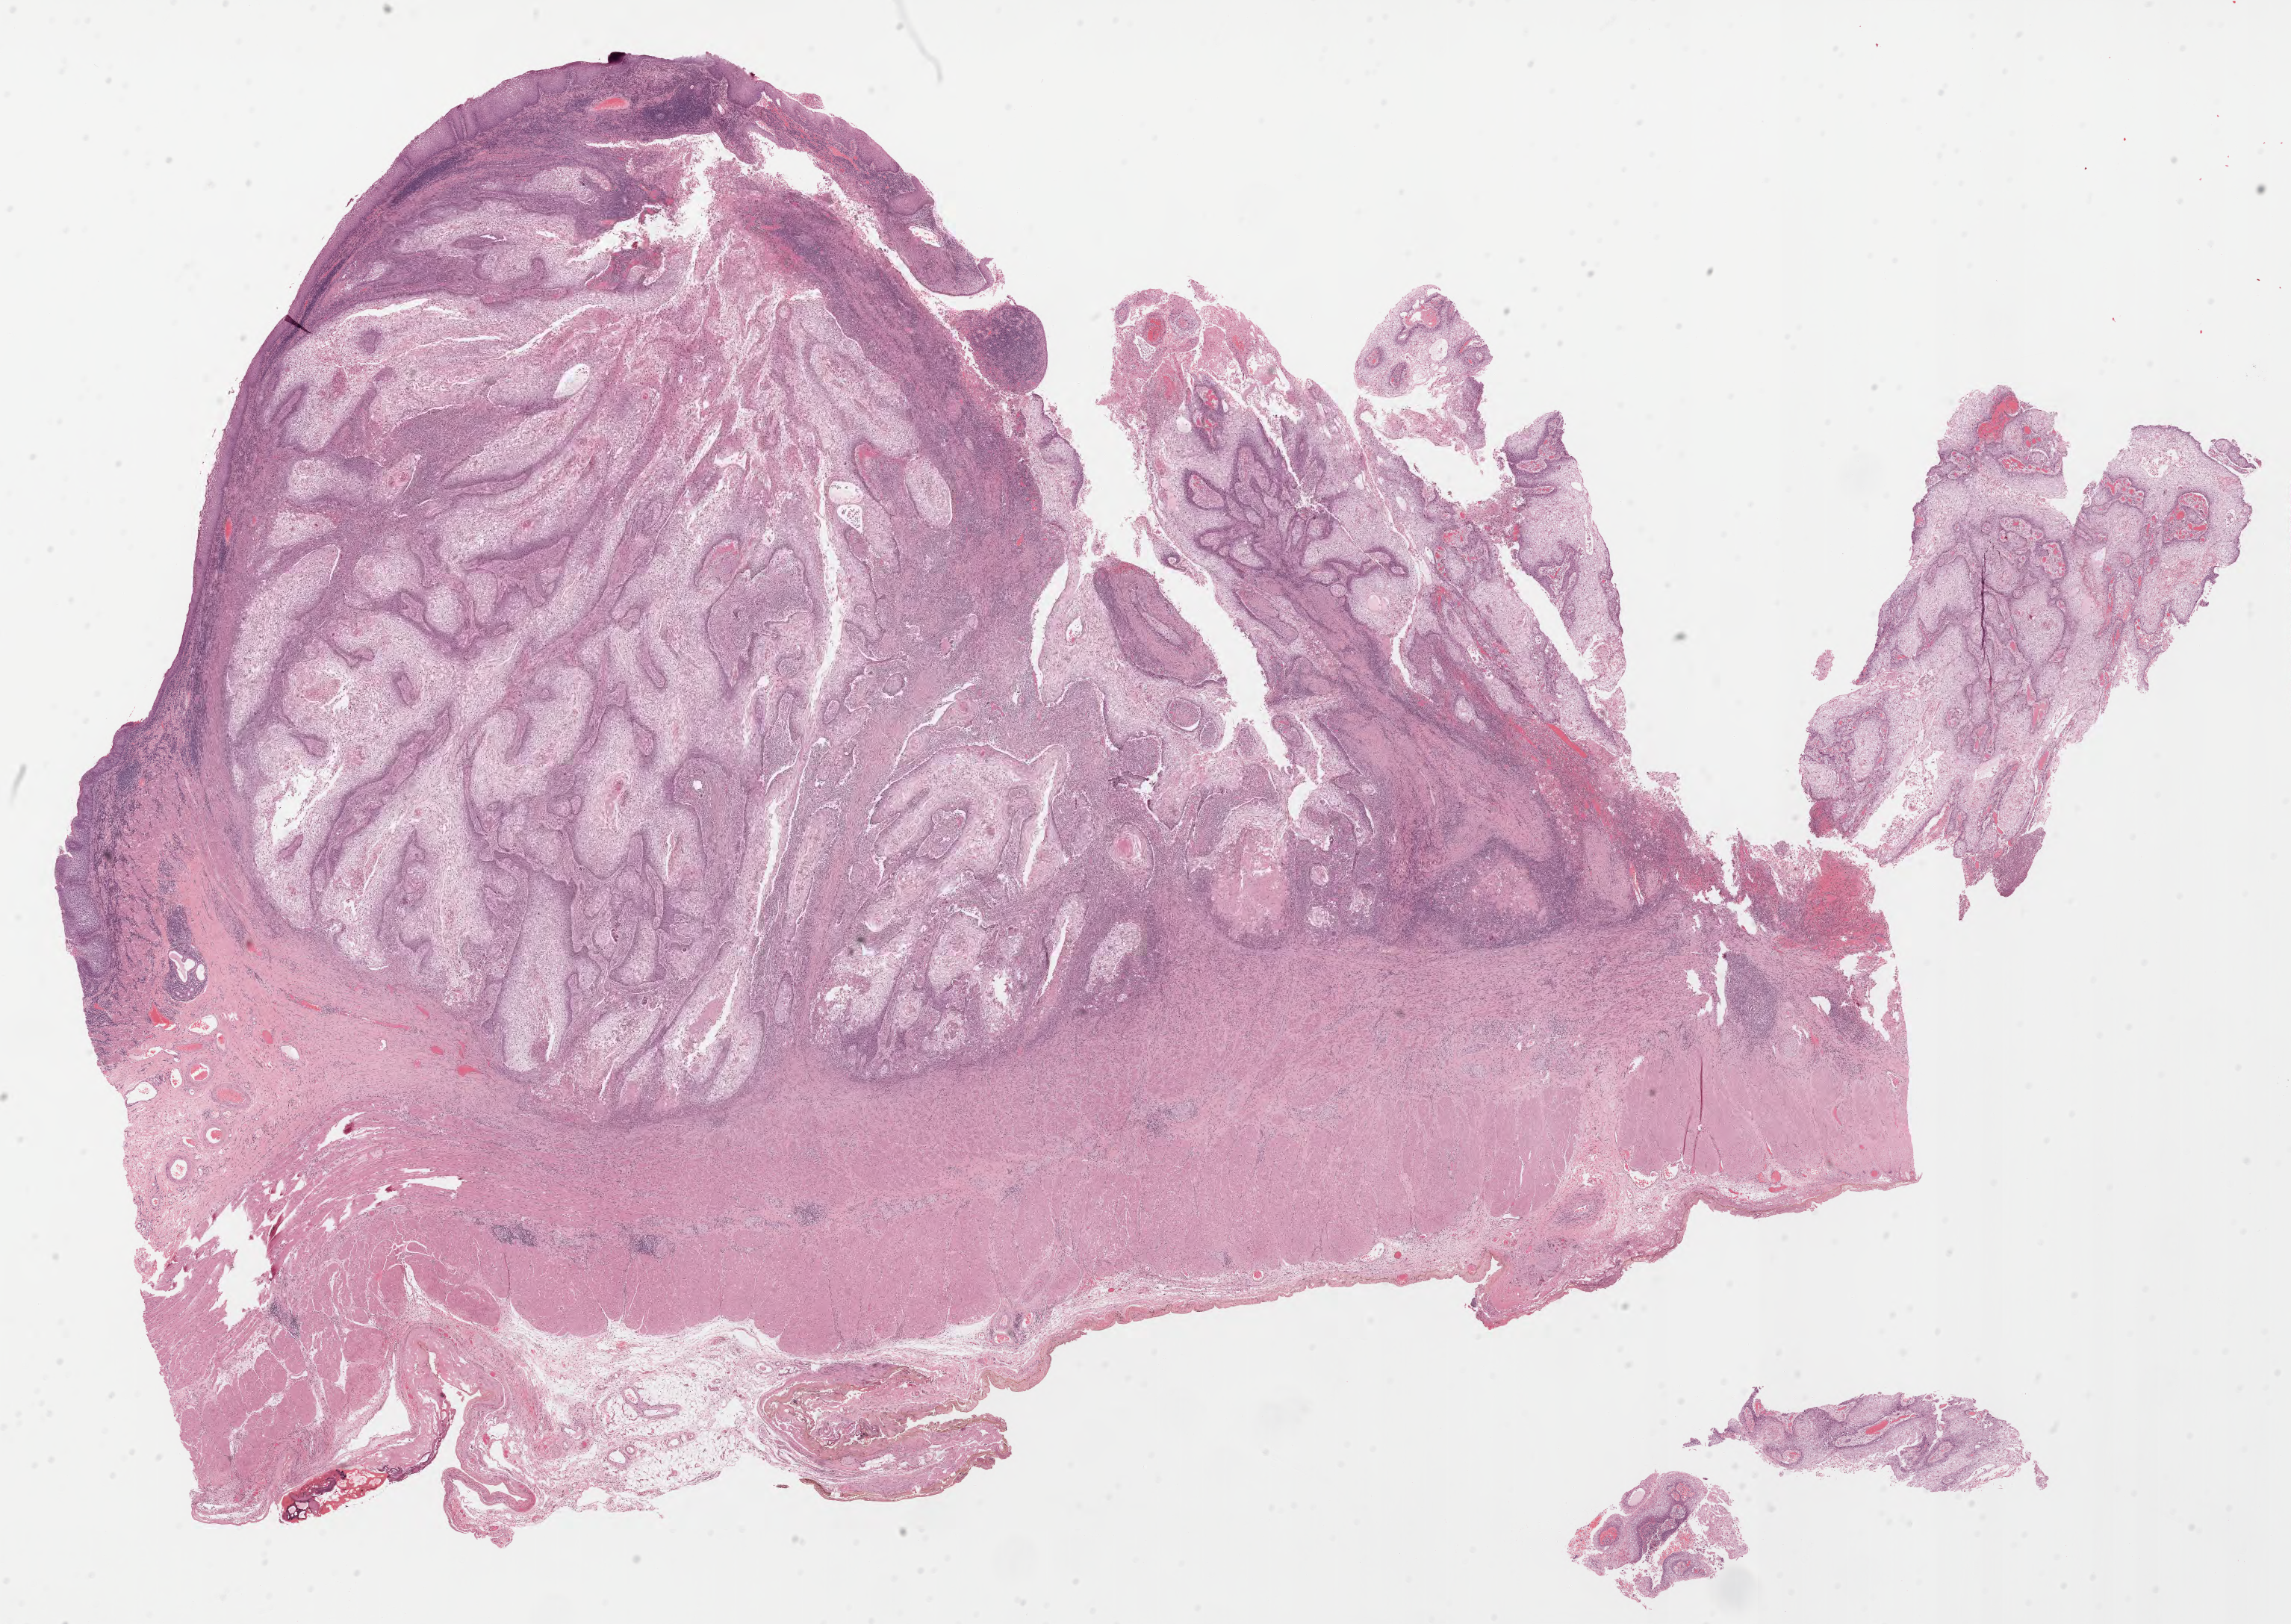
Hematoxylin and eosin (H&E) stained whole-slide image, shown as a low-resolution overview of the whole scanned area (about 24.7 x 17.5 mm), FFPE section, primary tumour sample from the esophagus. Patient: female, age at initial diagnosis 58 years. Histologic grade: G1 (well differentiated).
• TNM: T2 N0 M0
• AJCC pathologic stage: IB (7th edition)
• diagnosis: Squamous cell carcinoma, NOS (lower third of esophagus)